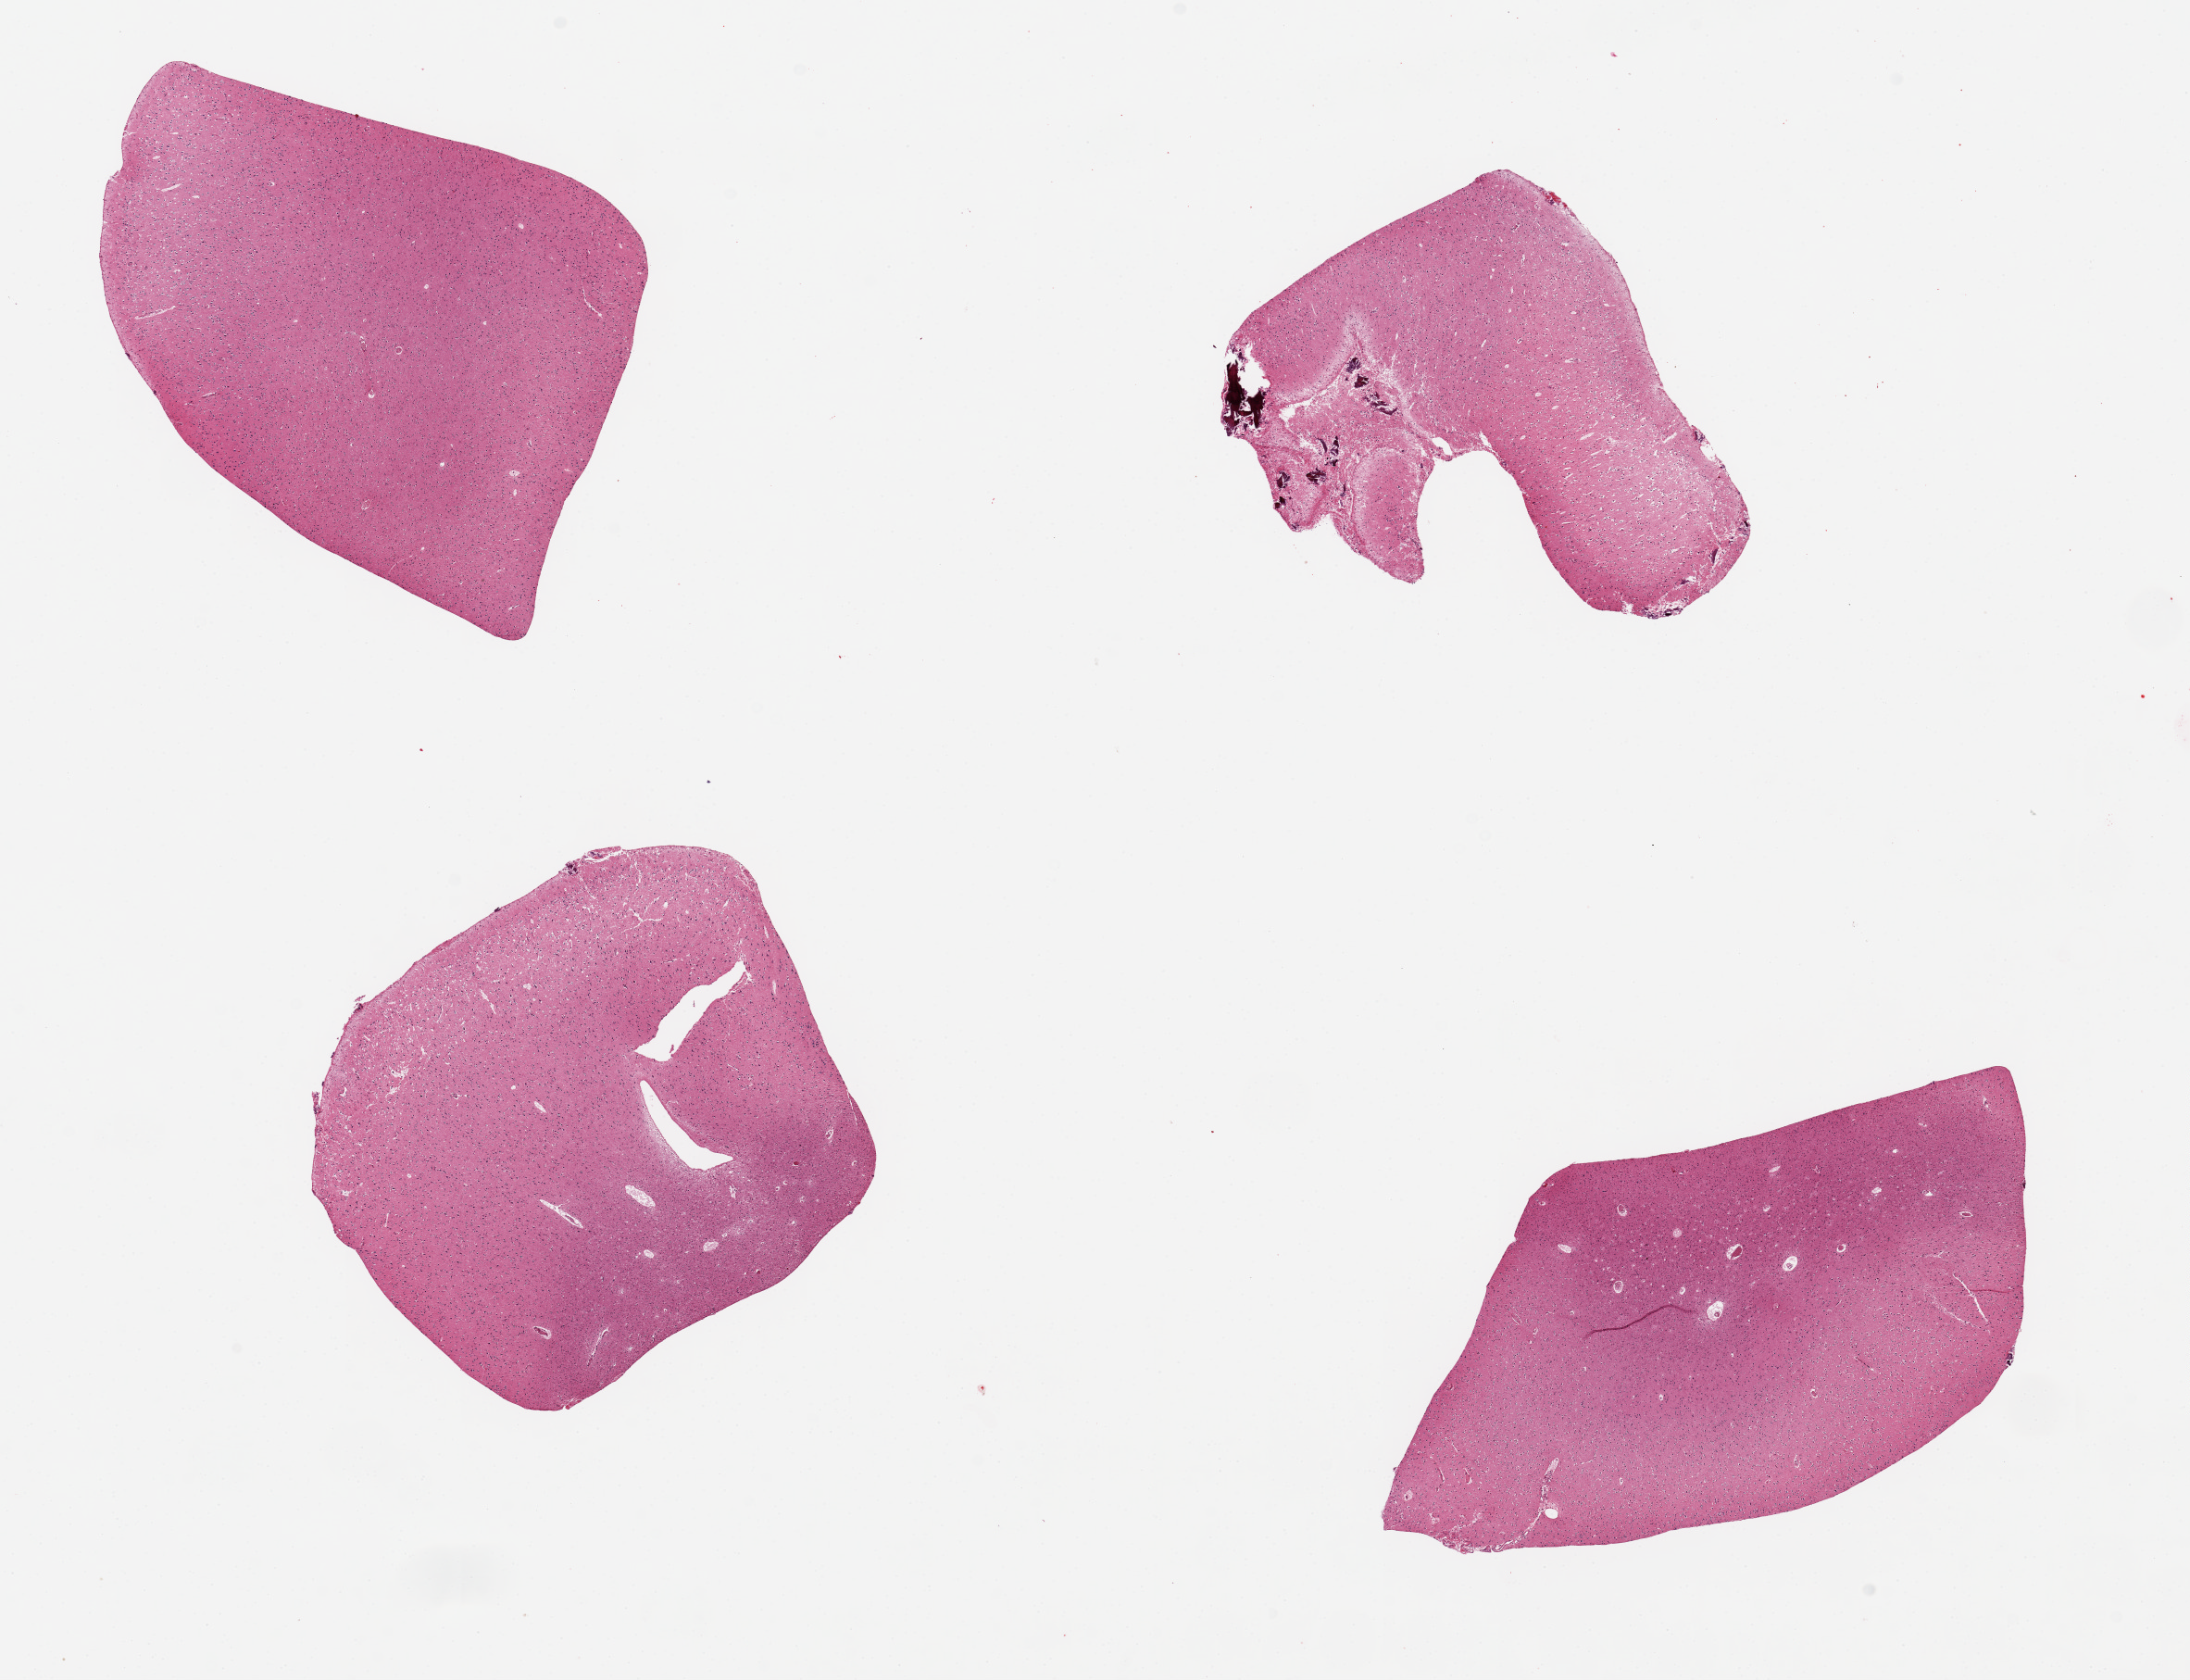
Whole-slide image, H&E stain, brightfield — a low-resolution overview of the entire scanned area, about 18.7 x 14.3 mm, PAXgene-fixed, paraffin-embedded tissue, sampled site (target tissue): cerebral cortex, tissue donor sample. Donor sex: male.
Pathologist's review note for this sample: 4 pieces, ~5x4mm.